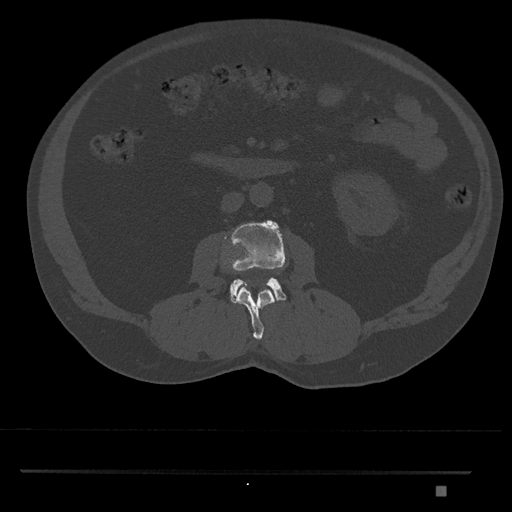
CT including the spine, one axial slice. Slice 717 of 1134 in the series (ordered by position). Reconstruction kernel Br40s/3. Bone window (W 1800 / L 400 HU). 512 × 512 image matrix, field of view 429 × 429 mm. Patient: male, 65 years. Case-level facts recorded for this patient, not image findings: primary cancer: prostate.
Annotated regions visible in this slice (semi-automatic segmentation, software-assisted and operator-edited):
- L2 vertebra: box from (x=236, y=286) to (x=275, y=340) px
- L3 vertebra: (x=225, y=220)–(x=287, y=304)